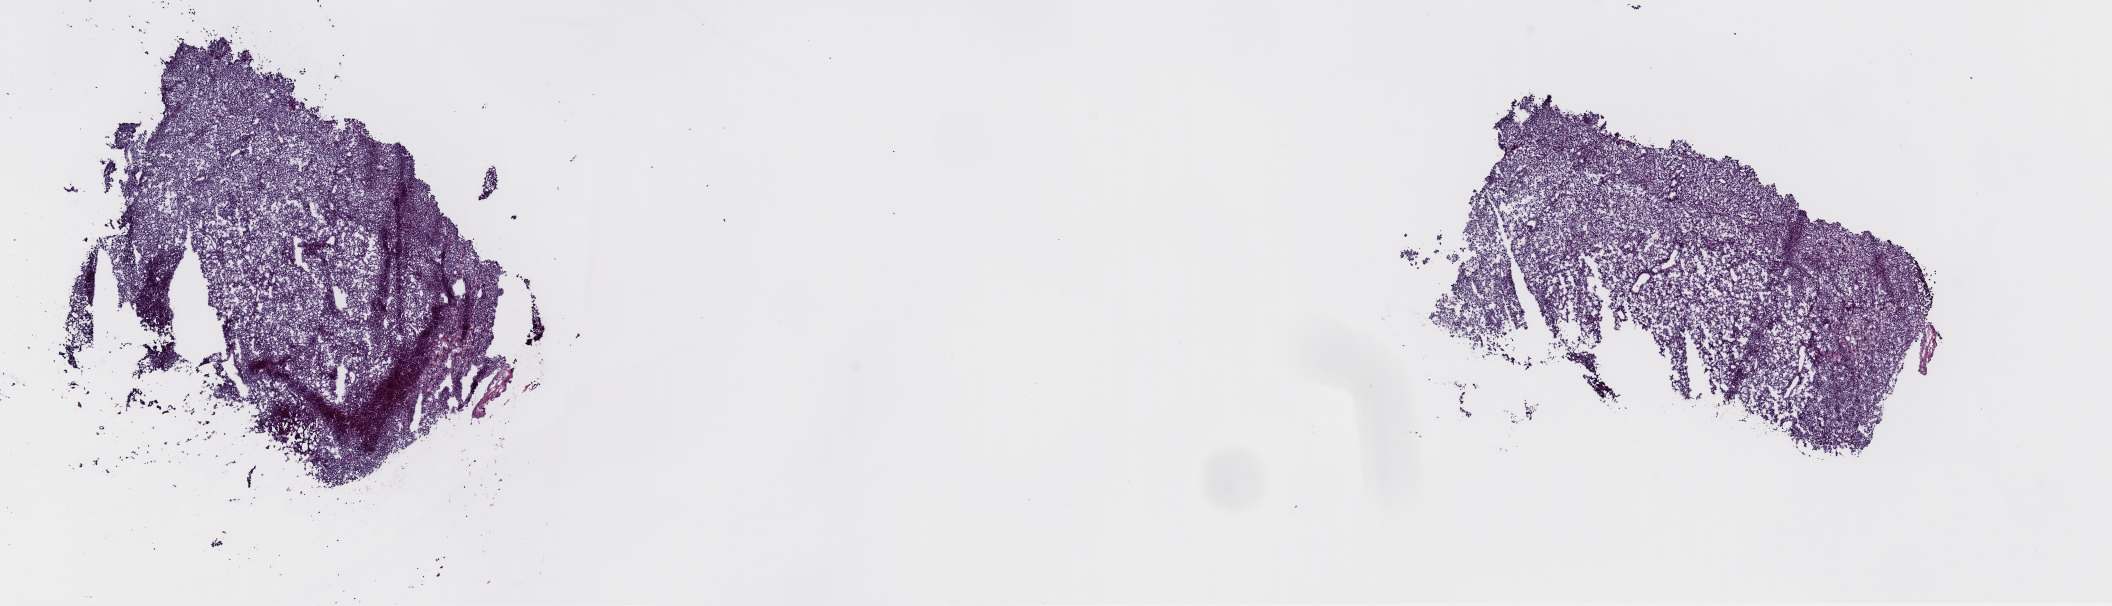
Whole-slide histology image, Hematoxylin and eosin (H&E) stained, shown as a low-resolution overview of the whole scanned area (about 16.7 x 4.8 mm, from a 40x scan); frozen section; metastatic tumour sample, sampled site not recorded. Patient: male, age at initial diagnosis 70 years. Composition of this section per pathologist review: tumour cells 100%, tumour nuclei 95%, normal cells 0%, stromal cells 0%, necrosis 0%. Inflammatory infiltration, as recorded: lymphocyte infiltration 1%, monocyte infiltration 0%, neutrophil infiltration 0%.
* this section: metastatic tumour tissue
* patient diagnosis: Malignant melanoma, NOS